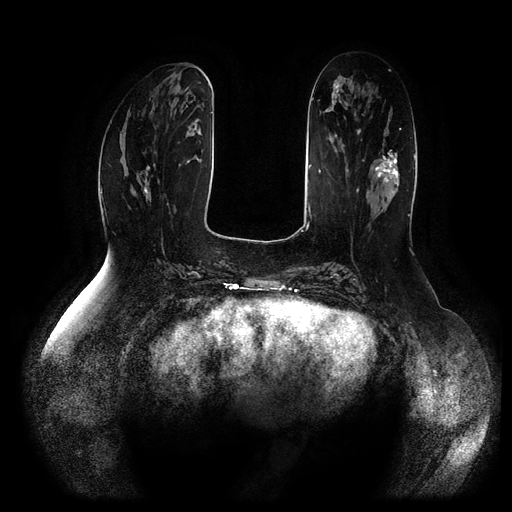
Breast MRI (dynamic contrast-enhanced, multi-phase), one axial slice. Position 37 of 116 along the scan axis. Dynamic contrast-enhanced series, time point 2 of 5 at this slice position (early post-contrast). 1.5 T. TE 2.5 ms, TR 5.2 ms. 512 × 512 image matrix, field of view 400 × 400 mm. Patient: female, 66 years.
Structures marked on this image (semi-automatic segmentation, software-assisted and operator-edited):
- breast lesion (labelled 'tumour' in the annotation; benign lesions carry a separate 'benign' label): bounding box <372,149,399,200> (left, top, right, bottom; pixels)